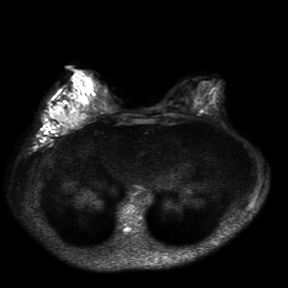
Breast MRI, one axial slice; slice 13 of 30 in the series (ordered by position); diffusion-weighted series; image 2 of 4 stored at this slice position (different b-values; order by instance number); 3 T; 4 mm slice thickness; 288 × 288 image matrix, field of view 360 × 360 mm. Female patient.
Outlined on this slice (outlined manually by an expert reader):
- tumour on diffusion-weighted imaging: bounding box <52,105,65,121> (left, top, right, bottom; pixels)